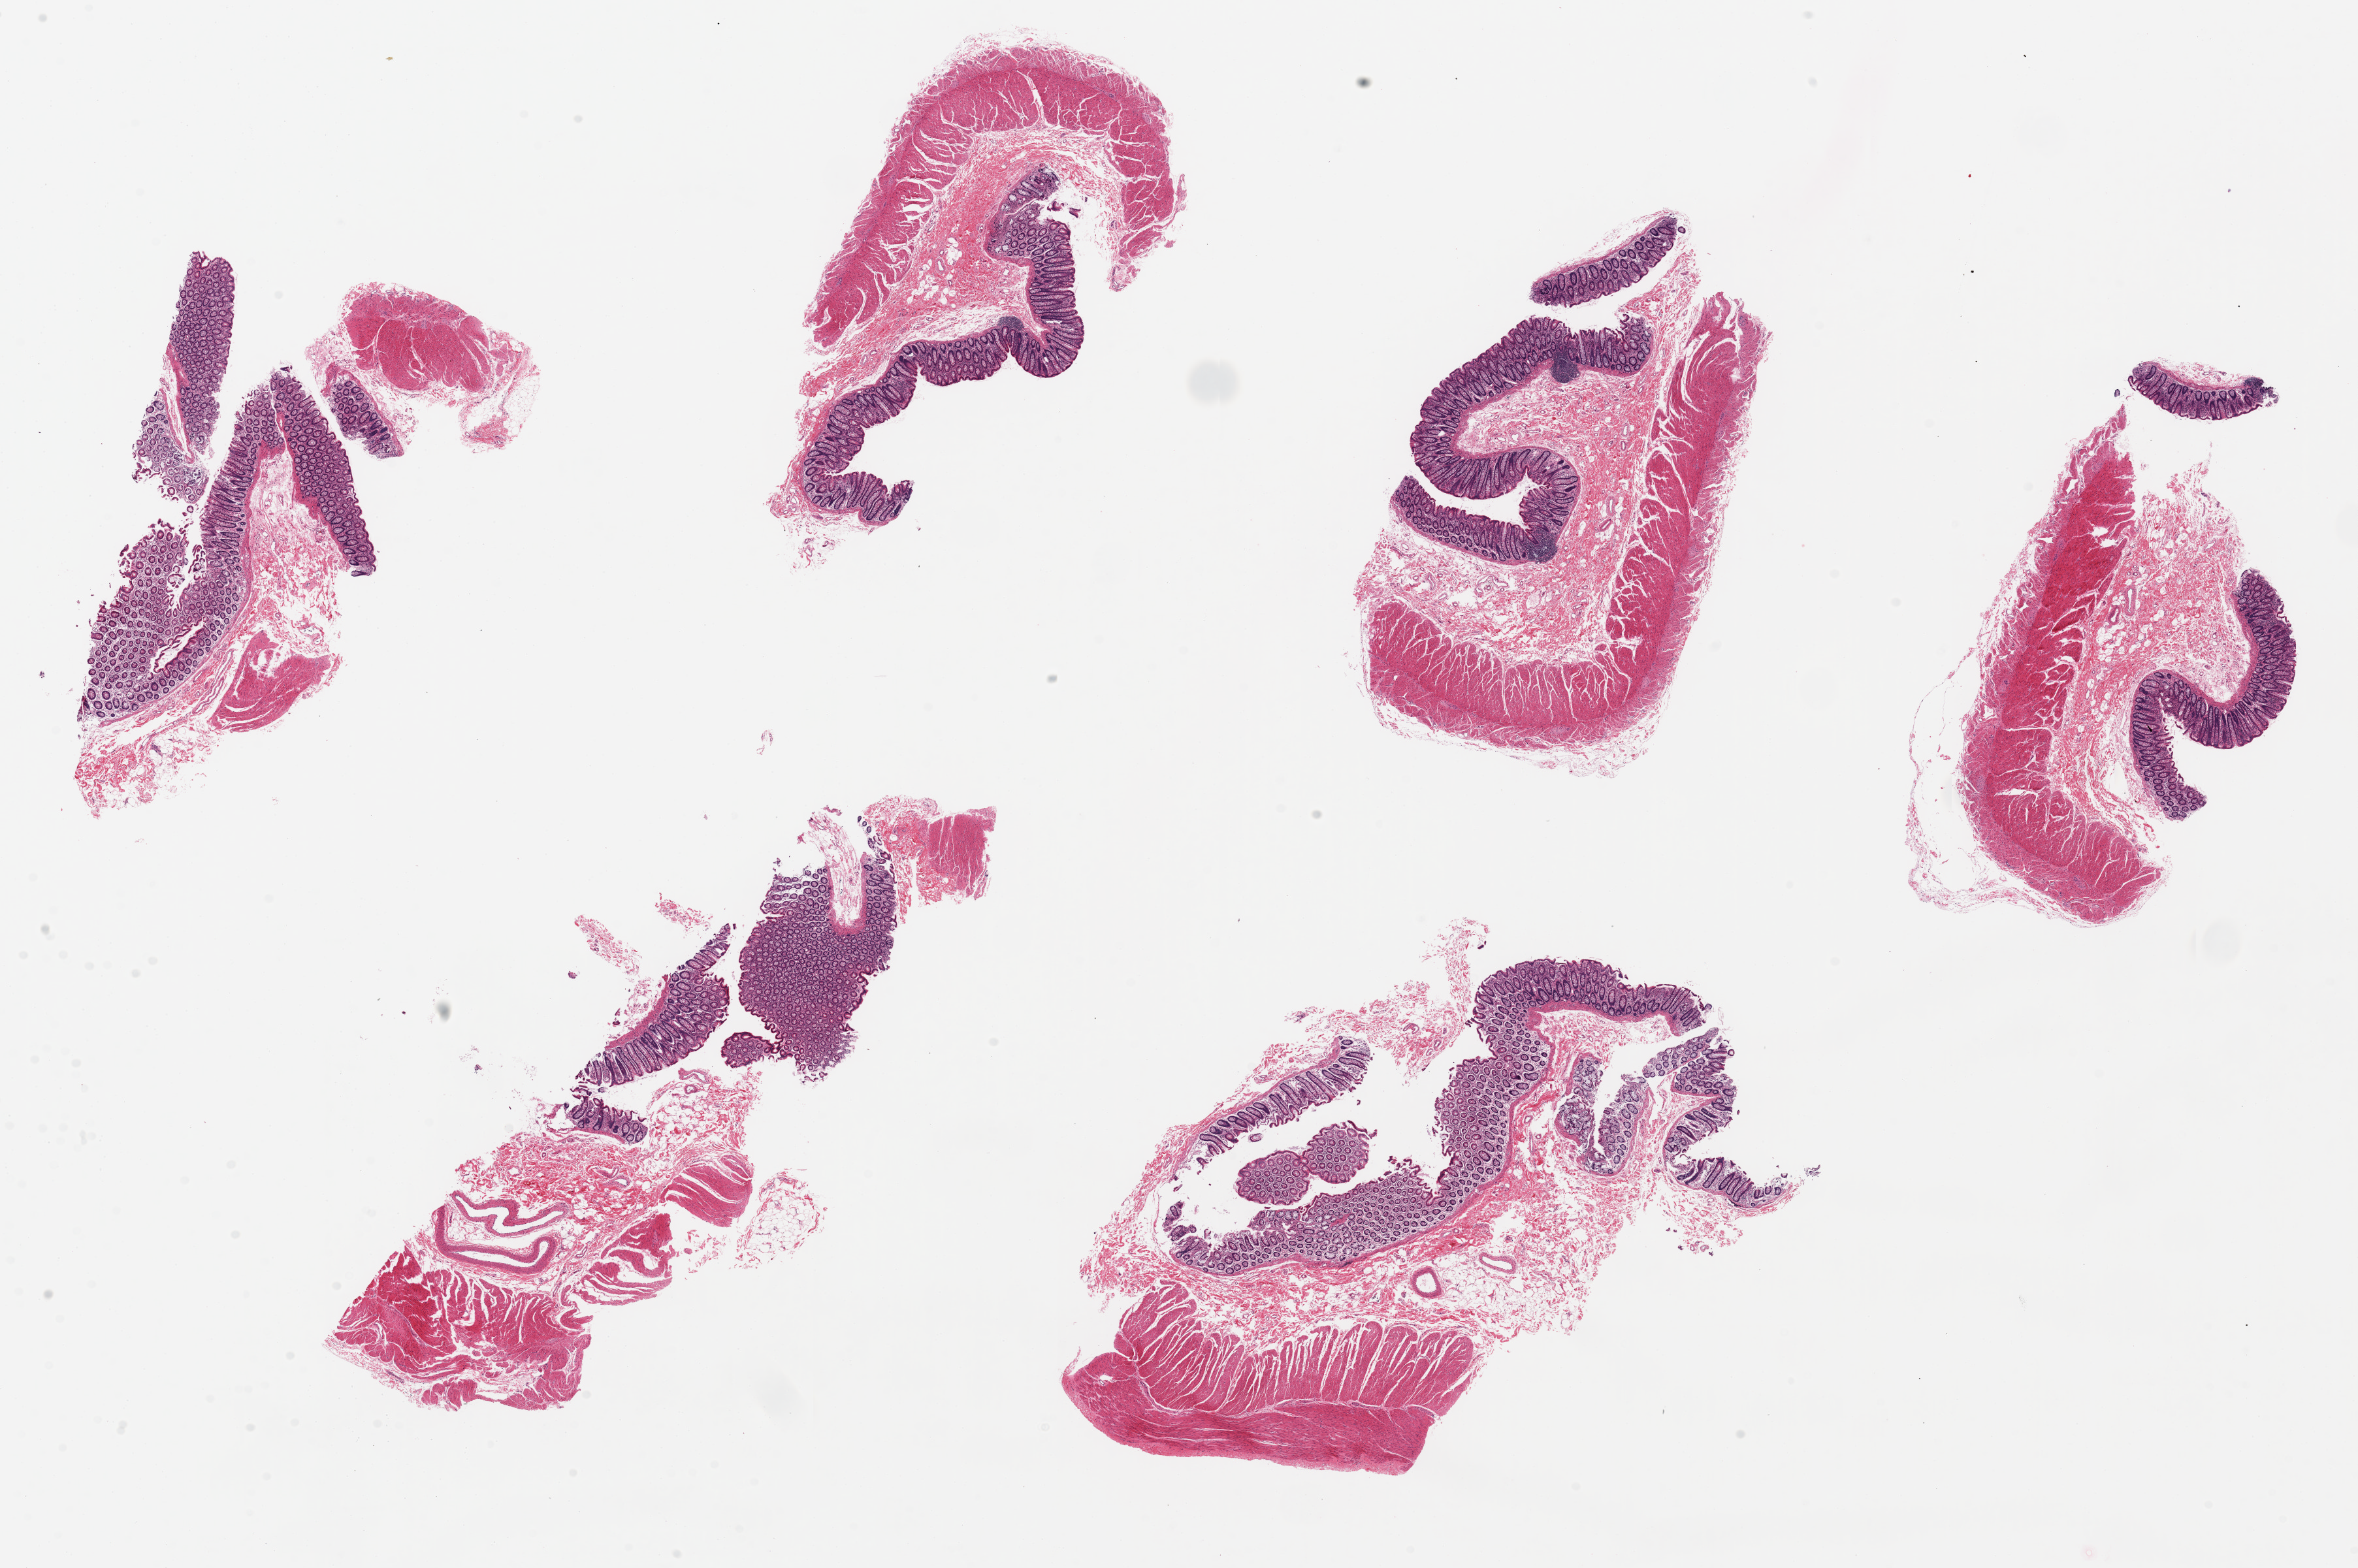
Digitized haematoxylin and eosin-stained section — a low-resolution overview of the entire scanned area, about 28.5 x 19.0 mm (slide scanned at 20x), PAXgene-fixed paraffin-embedded (PFPE) section, sampled site (target tissue): transverse colon, donor tissue sample.
• reviewer comment on this tissue sample: 7 pieces, up to 10x4.5mm; all have full thickness of wall